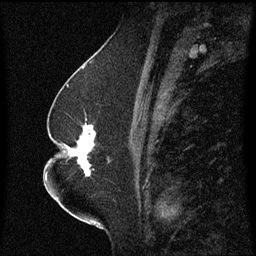
Breast MRI (dynamic contrast-enhanced), one sagittal slice. Slice 30 of 60 in the series (ordered by position). Dynamic contrast-enhanced series, image 2 of 3 at this slice position (ordered by acquisition). 1.5 T. TE 4.2 ms, TR 8.4 ms. 2.3 mm slice thickness. 256 × 256 image matrix, field of view 200 × 200 mm. Patient: female, 52 years. Case-level facts recorded for this patient, not image findings: setting: breast cancer imaged before/during neoadjuvant chemotherapy; receptor status: HR-positive, HER2-negative.
Structures marked on this image (semi-automatic segmentation, software-assisted and operator-edited):
- analysis volume of interest (the breast-tissue region the enhancement analysis was run in; not a lesion): box from (x=65, y=126) to (x=111, y=177) px
- tumour enhancement mask (voxels above the 70 % enhancement threshold inside the analysis volume of interest): (x=68, y=126)–(x=96, y=177)